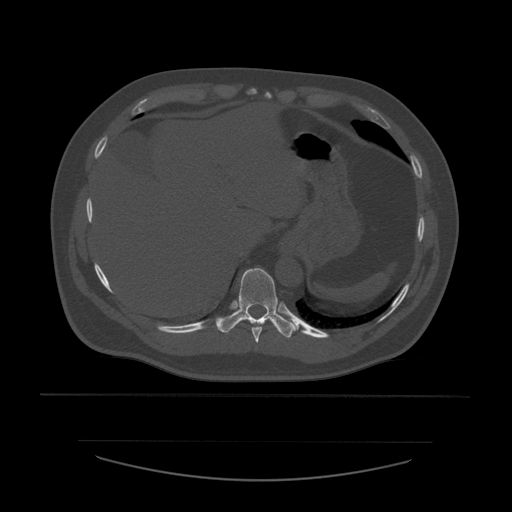
CT including the spine, one axial slice. Slice 303 of 532 in the series (ordered by position). Reconstruction kernel STANDARD. 120 kVp. Bone window (W 1800 / L 400 HU). 512 × 512 image matrix. Patient age 44 years. Case-level facts recorded for this patient, not image findings: primary cancer: soft tissue sarcoma.
Annotated regions visible in this slice (semi-automatic segmentation, software-assisted and operator-edited):
- T10 vertebra: box from (x=216, y=268) to (x=298, y=338) px
- T9 vertebra: (x=252, y=322)–(x=274, y=343)